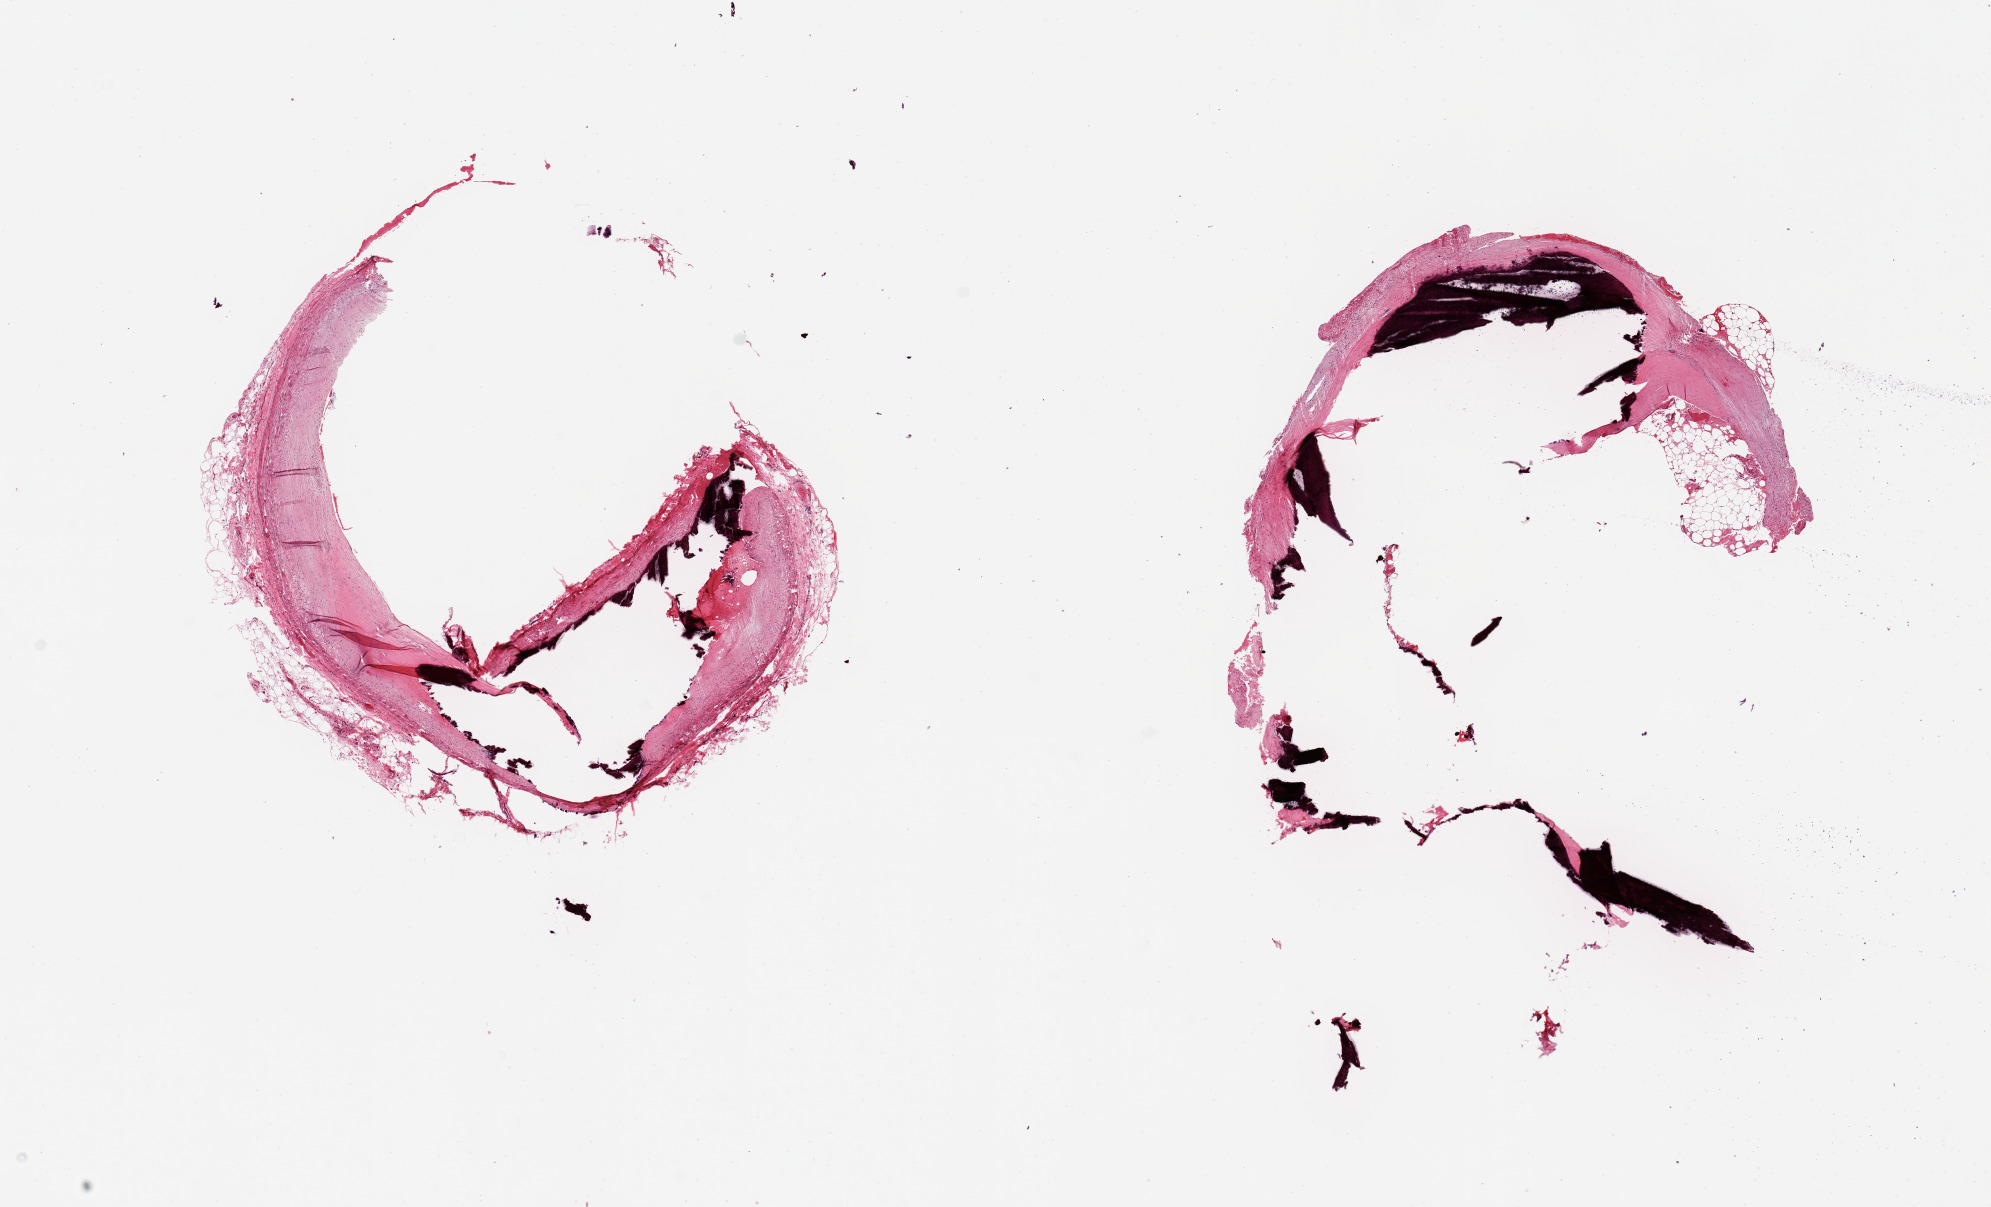
Digitized H&E-stained section, shown as a low-resolution overview of the whole scanned area (about 15.8 x 9.5 mm), PAXgene-fixed paraffin-embedded (PFPE) section, sampled site (target tissue): coronary artery, donor tissue sample. Donor sex: female.
• reviewer comment on this tissue sample: 2 pieces; extensive calcified atherosclerosis with little residual normal arterial content